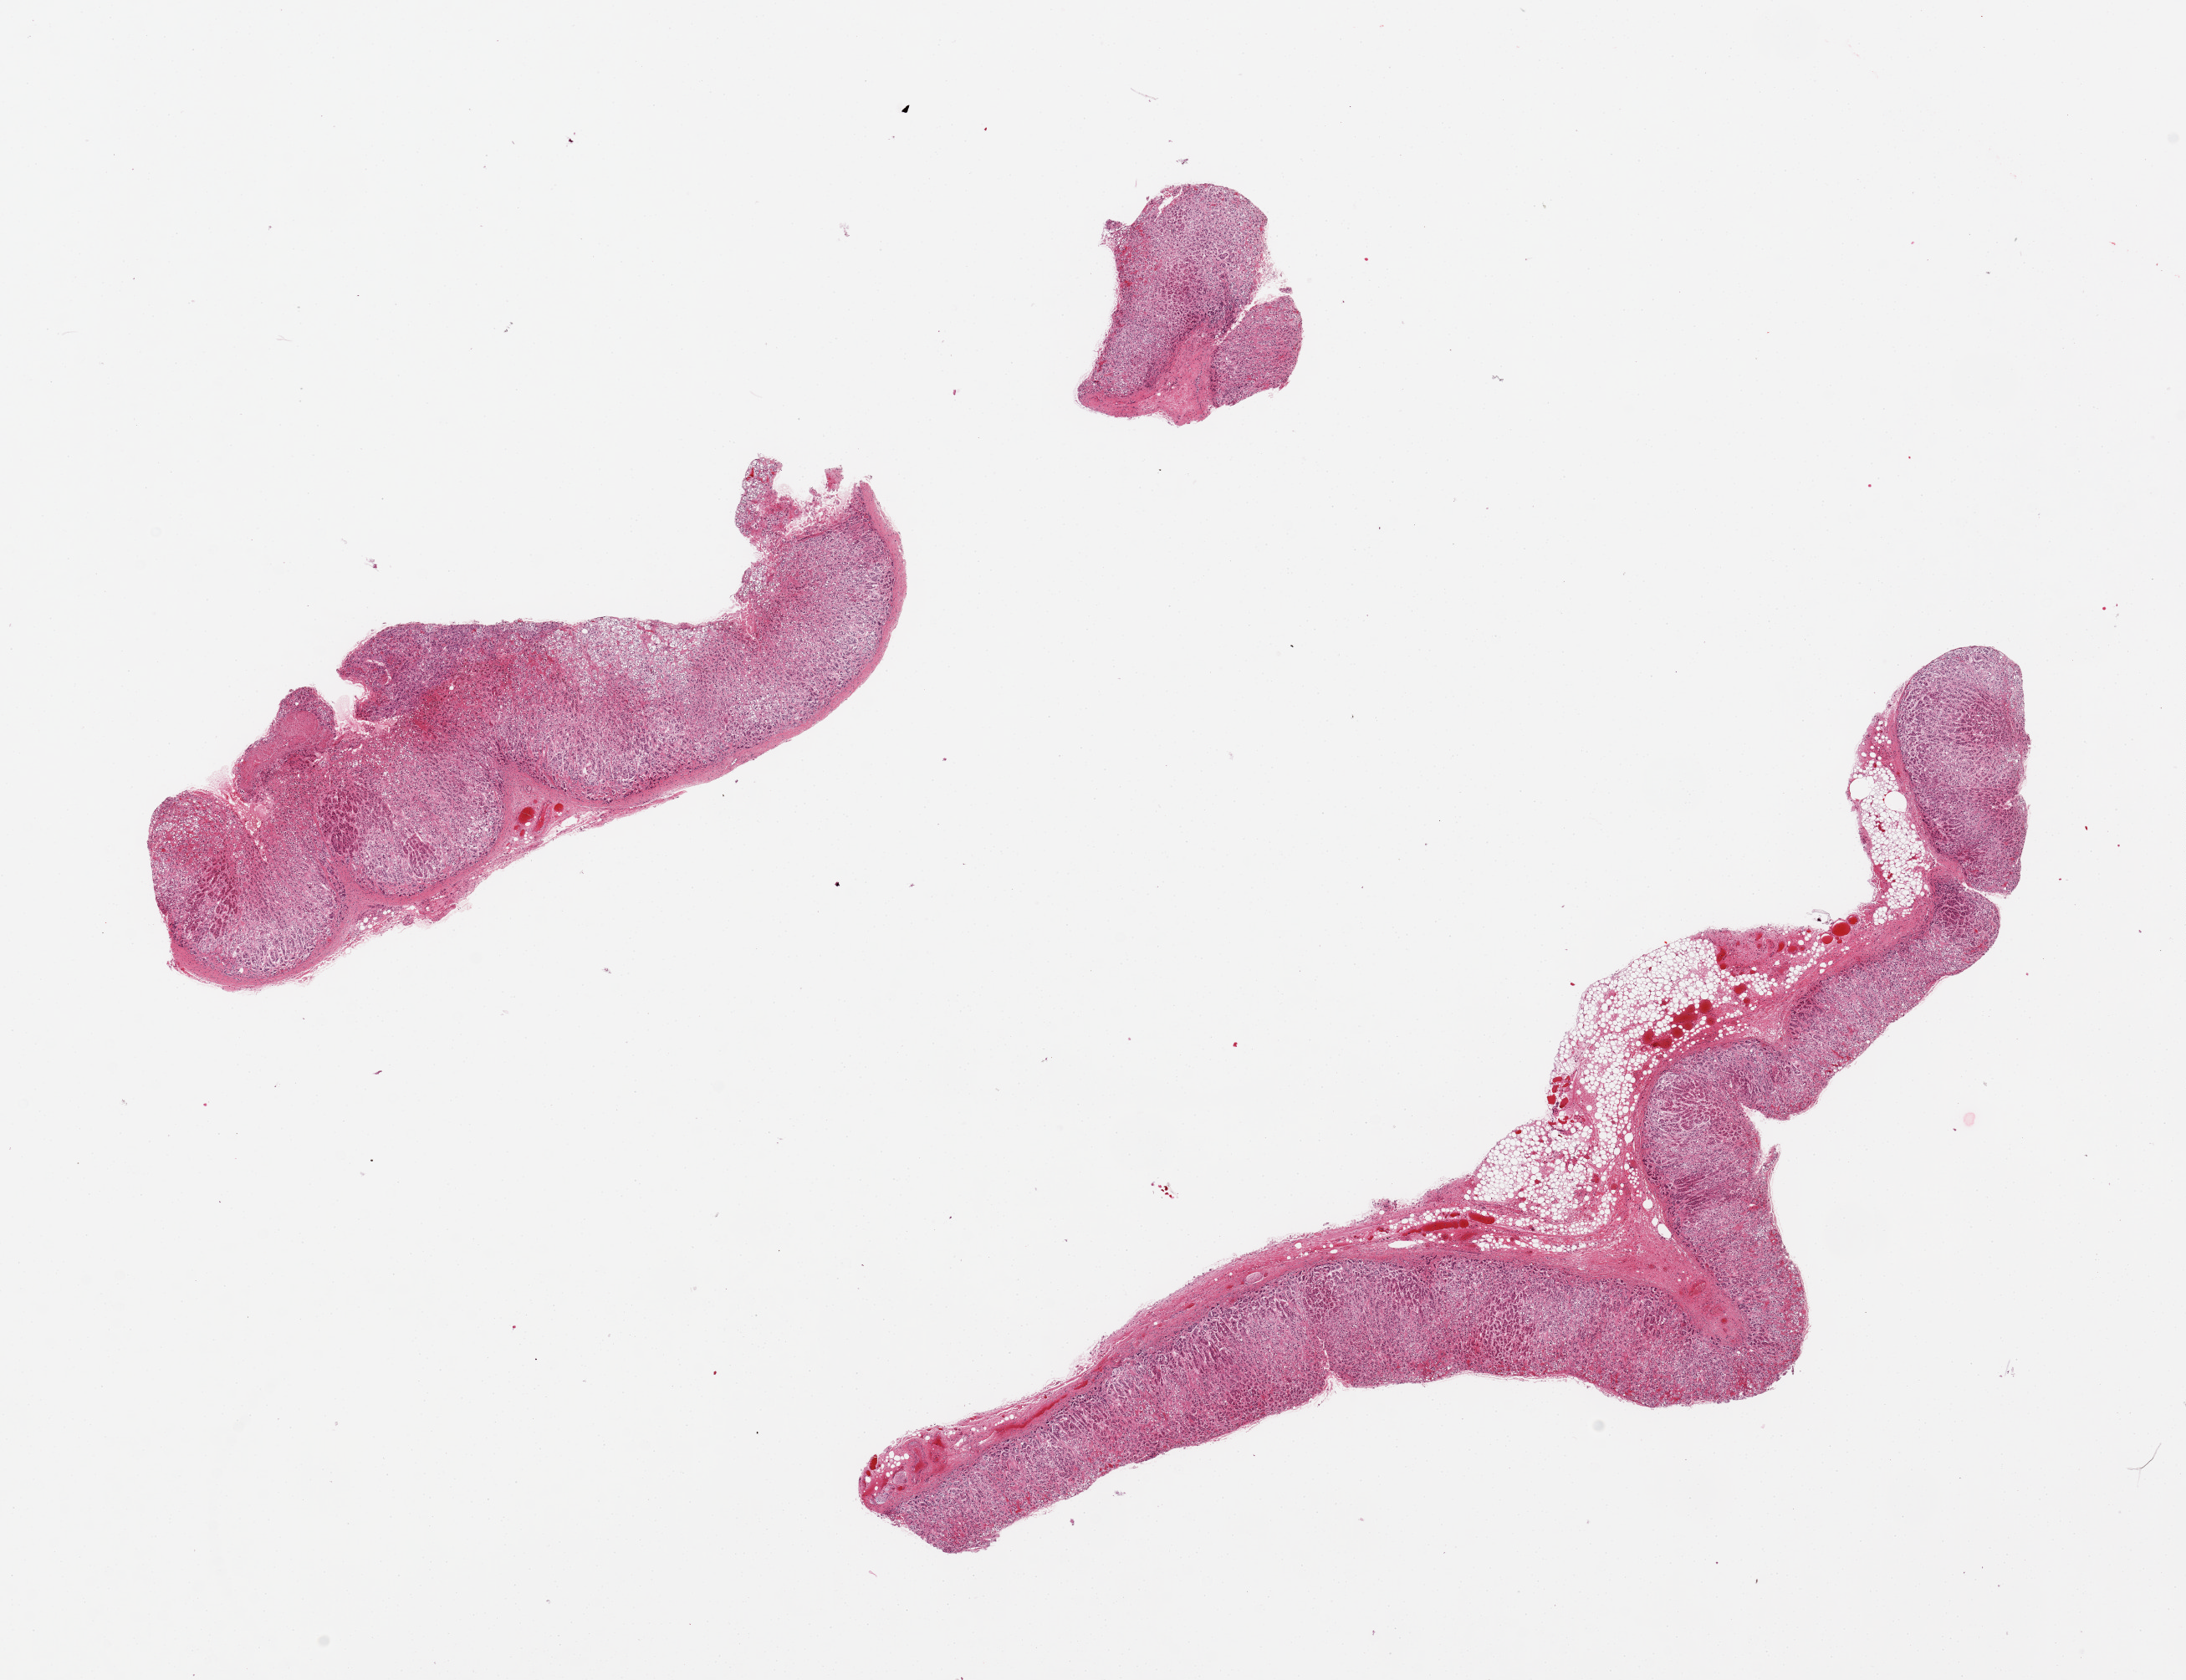
Hematoxylin and eosin (H&E) whole-slide image, low-resolution overview of the scanned area, about 20.7 x 15.9 mm (acquisition: 20x scan), PAXgene-fixed paraffin-embedded (PFPE) section, target tissue: adrenal gland, tissue donor sample. Female donor.
Pathologist's review note for this sample: 2 pieces, all cortex, badly autolyzed.